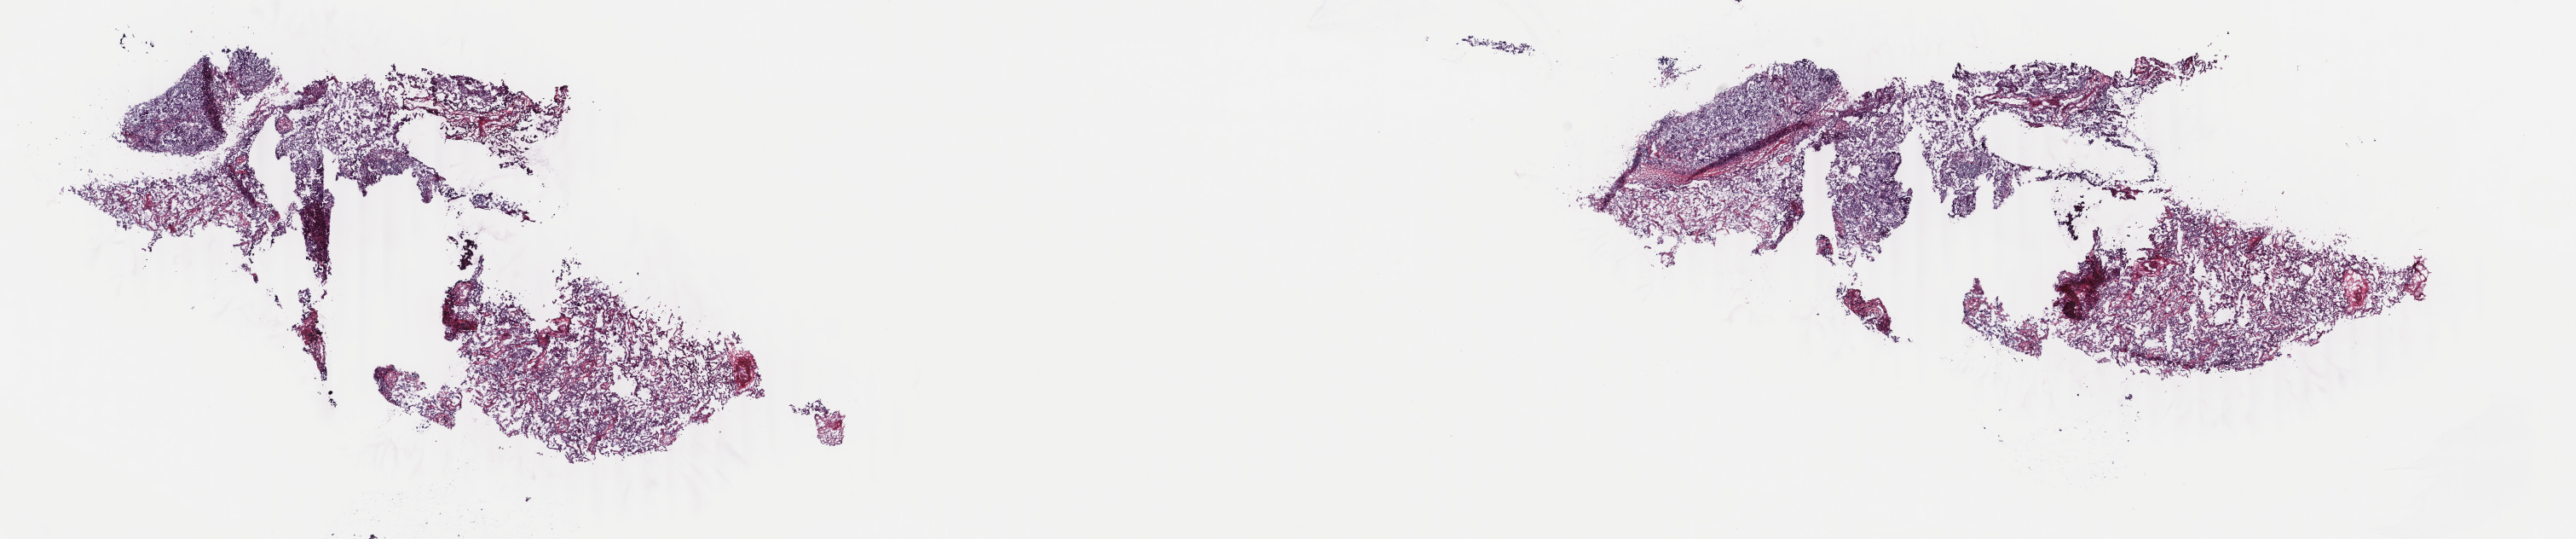
H&E-stained whole-slide image, shown as a low-resolution overview of the whole scanned area (about 24.0 x 5.0 mm, acquisition: 40x scan); frozen section from the top of the tissue portion; primary tumour sample from the lung. Patient: male, age at initial diagnosis 66 years. Composition of this section per pathologist review: tumour cells 95%, tumour nuclei 65%, normal cells 0%, stromal cells 0%, necrosis 5%. Inflammatory infiltration, as recorded: lymphocyte infiltration 10%, monocyte infiltration 2%, neutrophil infiltration 1%.
AJCC pathologic stage: IA. Pathologic diagnosis: Adenocarcinoma with mixed subtypes (middle lobe, lung). Laterality: right.